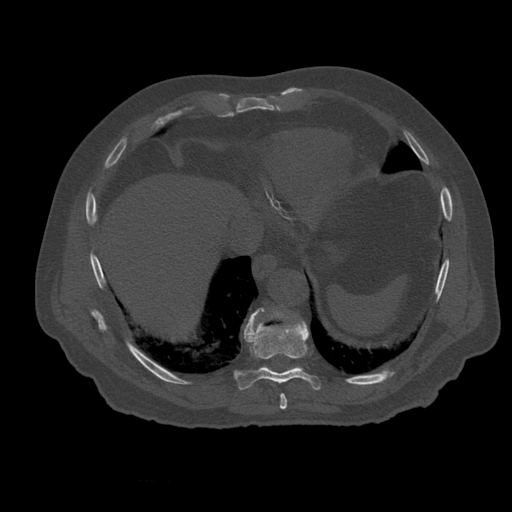
CT including the spine, one axial slice. Position 320 of 399 along the scan axis. 120 kVp. Bone window (W 1800 / L 400 HU). 512 × 512 image matrix, field of view 407 × 407 mm. Patient age 73 years. Case-level facts recorded for this patient, not image findings: primary cancer: prostate; vertebrae with lytic lesions (as recorded): L2.
Outlined on this slice (semi-automatically segmented with operator editing):
- T10 vertebra: bounding box <270,311,303,369> (left, top, right, bottom; pixels)
- T8 vertebra: <280,394,288,410>
- T9 vertebra: <235,309,321,391>